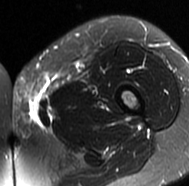
MRI of an extremity soft-tissue mass, one axial slice. Slice 21 of 77 in the series (ordered by position). T2-weighted fat-saturated. MR volume resampled by the dataset authors to the PET/CT grid (not the native acquisition matrix). 3.27 mm slice thickness. 189 × 186 image matrix. Female patient. Case-level facts recorded for this patient, not image findings: histological type: leiomyosarcoma; grade: high; site of the primary tumour: groin.
Annotated regions visible in this slice (expert contour drawn on MRI and transferred to this co-registered scan by the dataset authors):
- gross tumour volume including surrounding oedema: bounding box (x1, y1, x2, y2) in pixels: (10, 75, 68, 126)